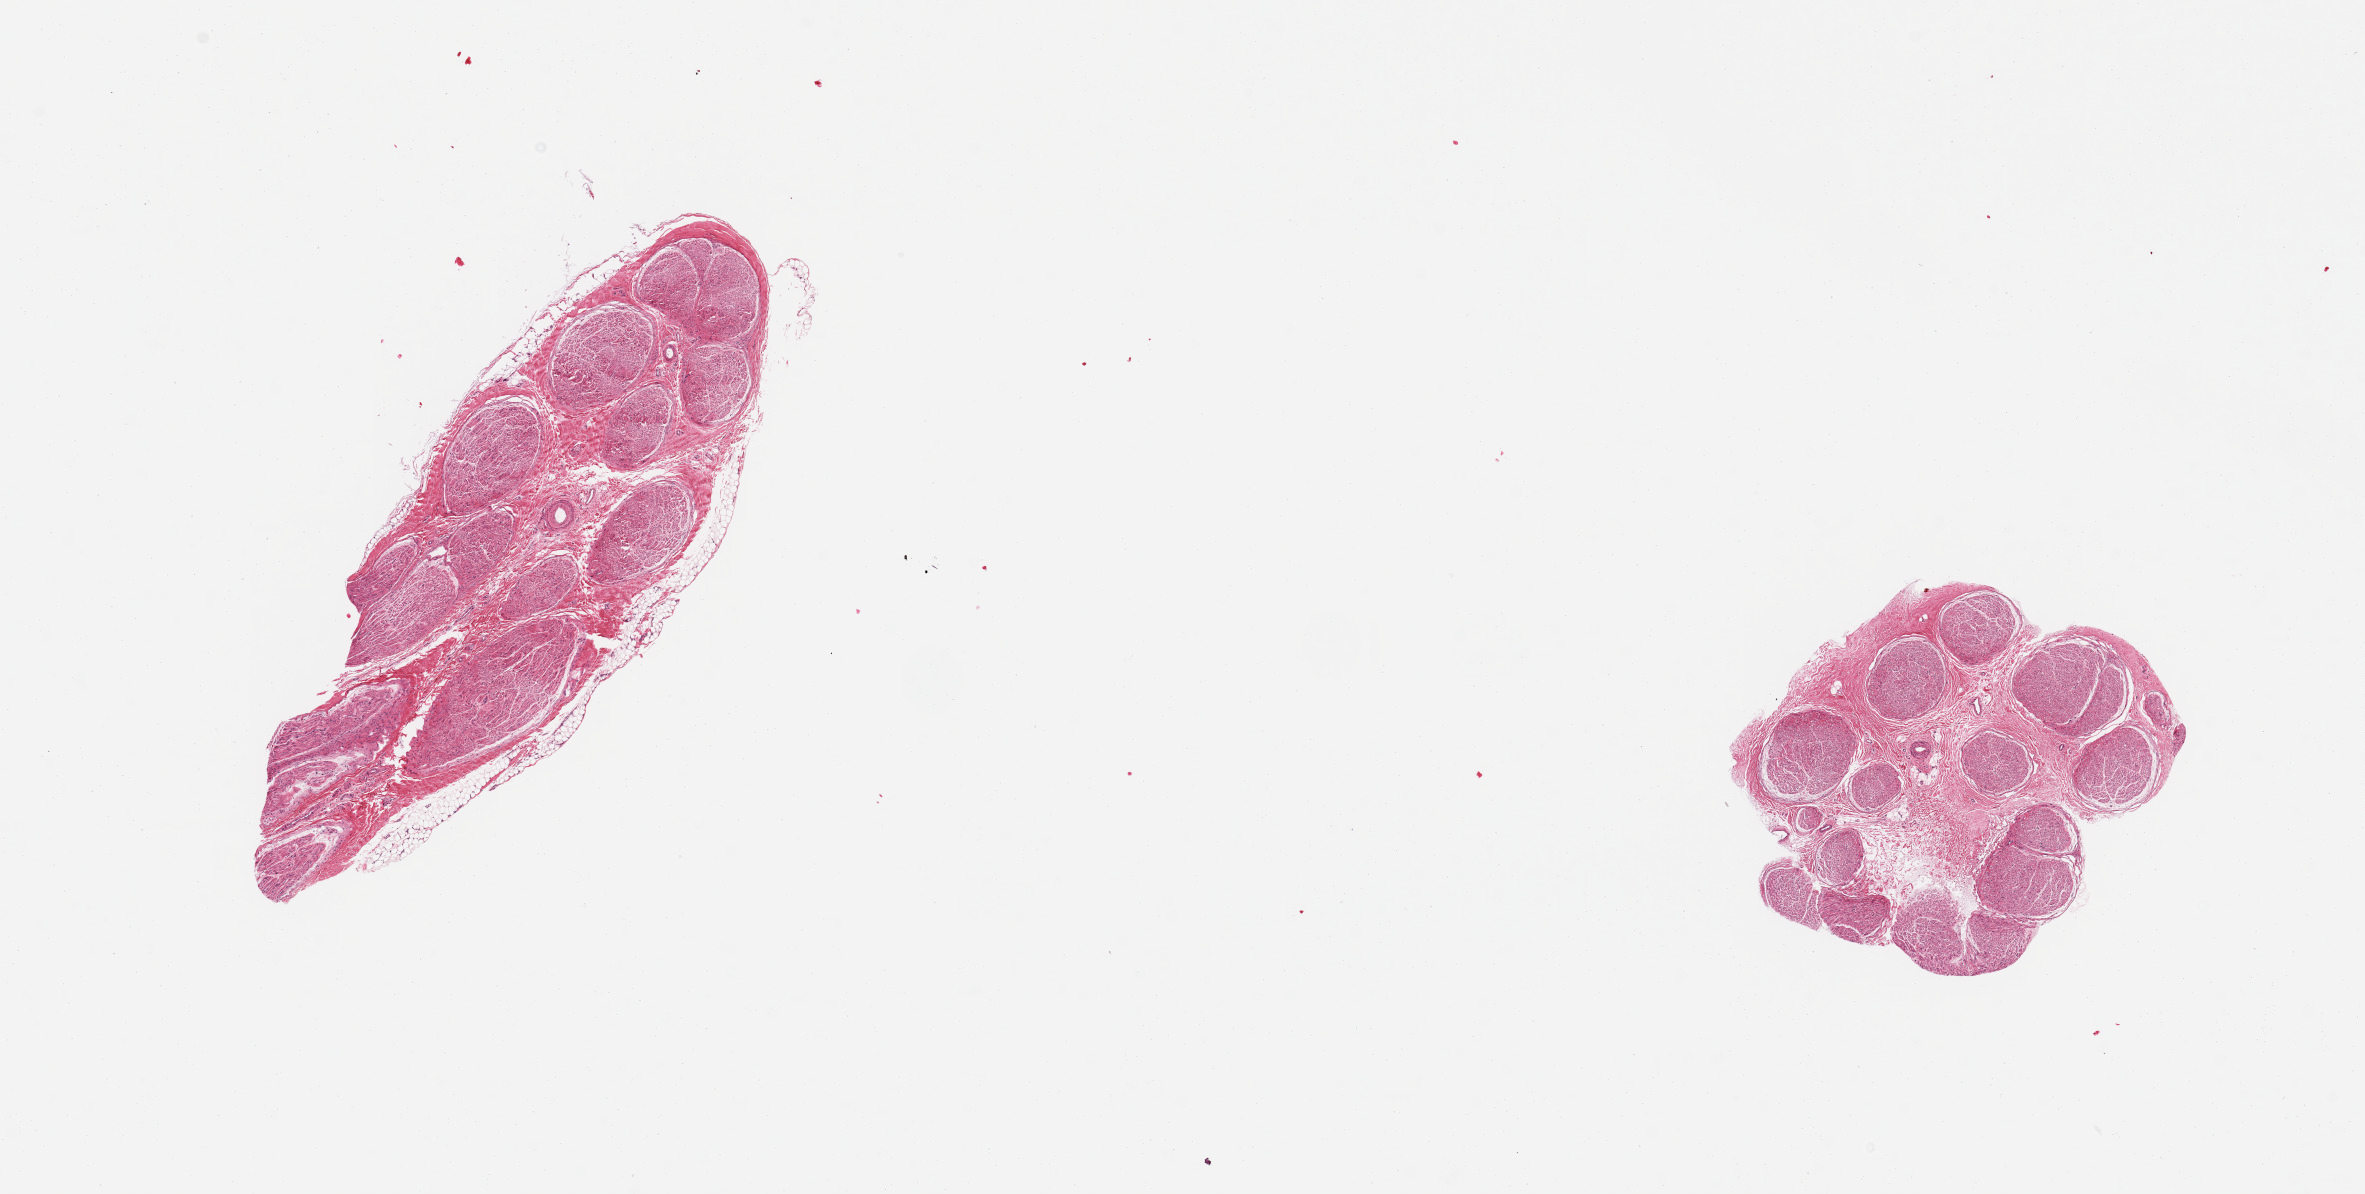
Hematoxylin and eosin (H&E) whole-slide image, shown as a low-resolution overview of the whole scanned area (about 18.7 x 9.4 mm); PAXgene-fixed paraffin-embedded (PFPE) section; target tissue: tibial nerve; donor tissue sample. Donor: male.
Review note (as recorded): 2 pieces, trace adherent fat.